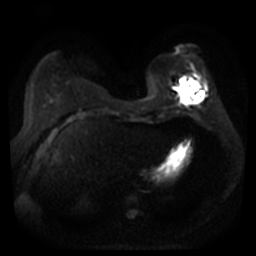
Breast MRI, one axial slice; position 11 of 44 along the scan axis; diffusion-weighted series; image 2 of 4 stored at this slice position (different b-values; order by instance number); 3 T; 256 × 256 image matrix. Female patient.
Annotated regions visible in this slice (outlined manually by an expert reader):
- tumour on diffusion-weighted imaging: bounding box [x1, y1, x2, y2] px = [177, 79, 201, 104]